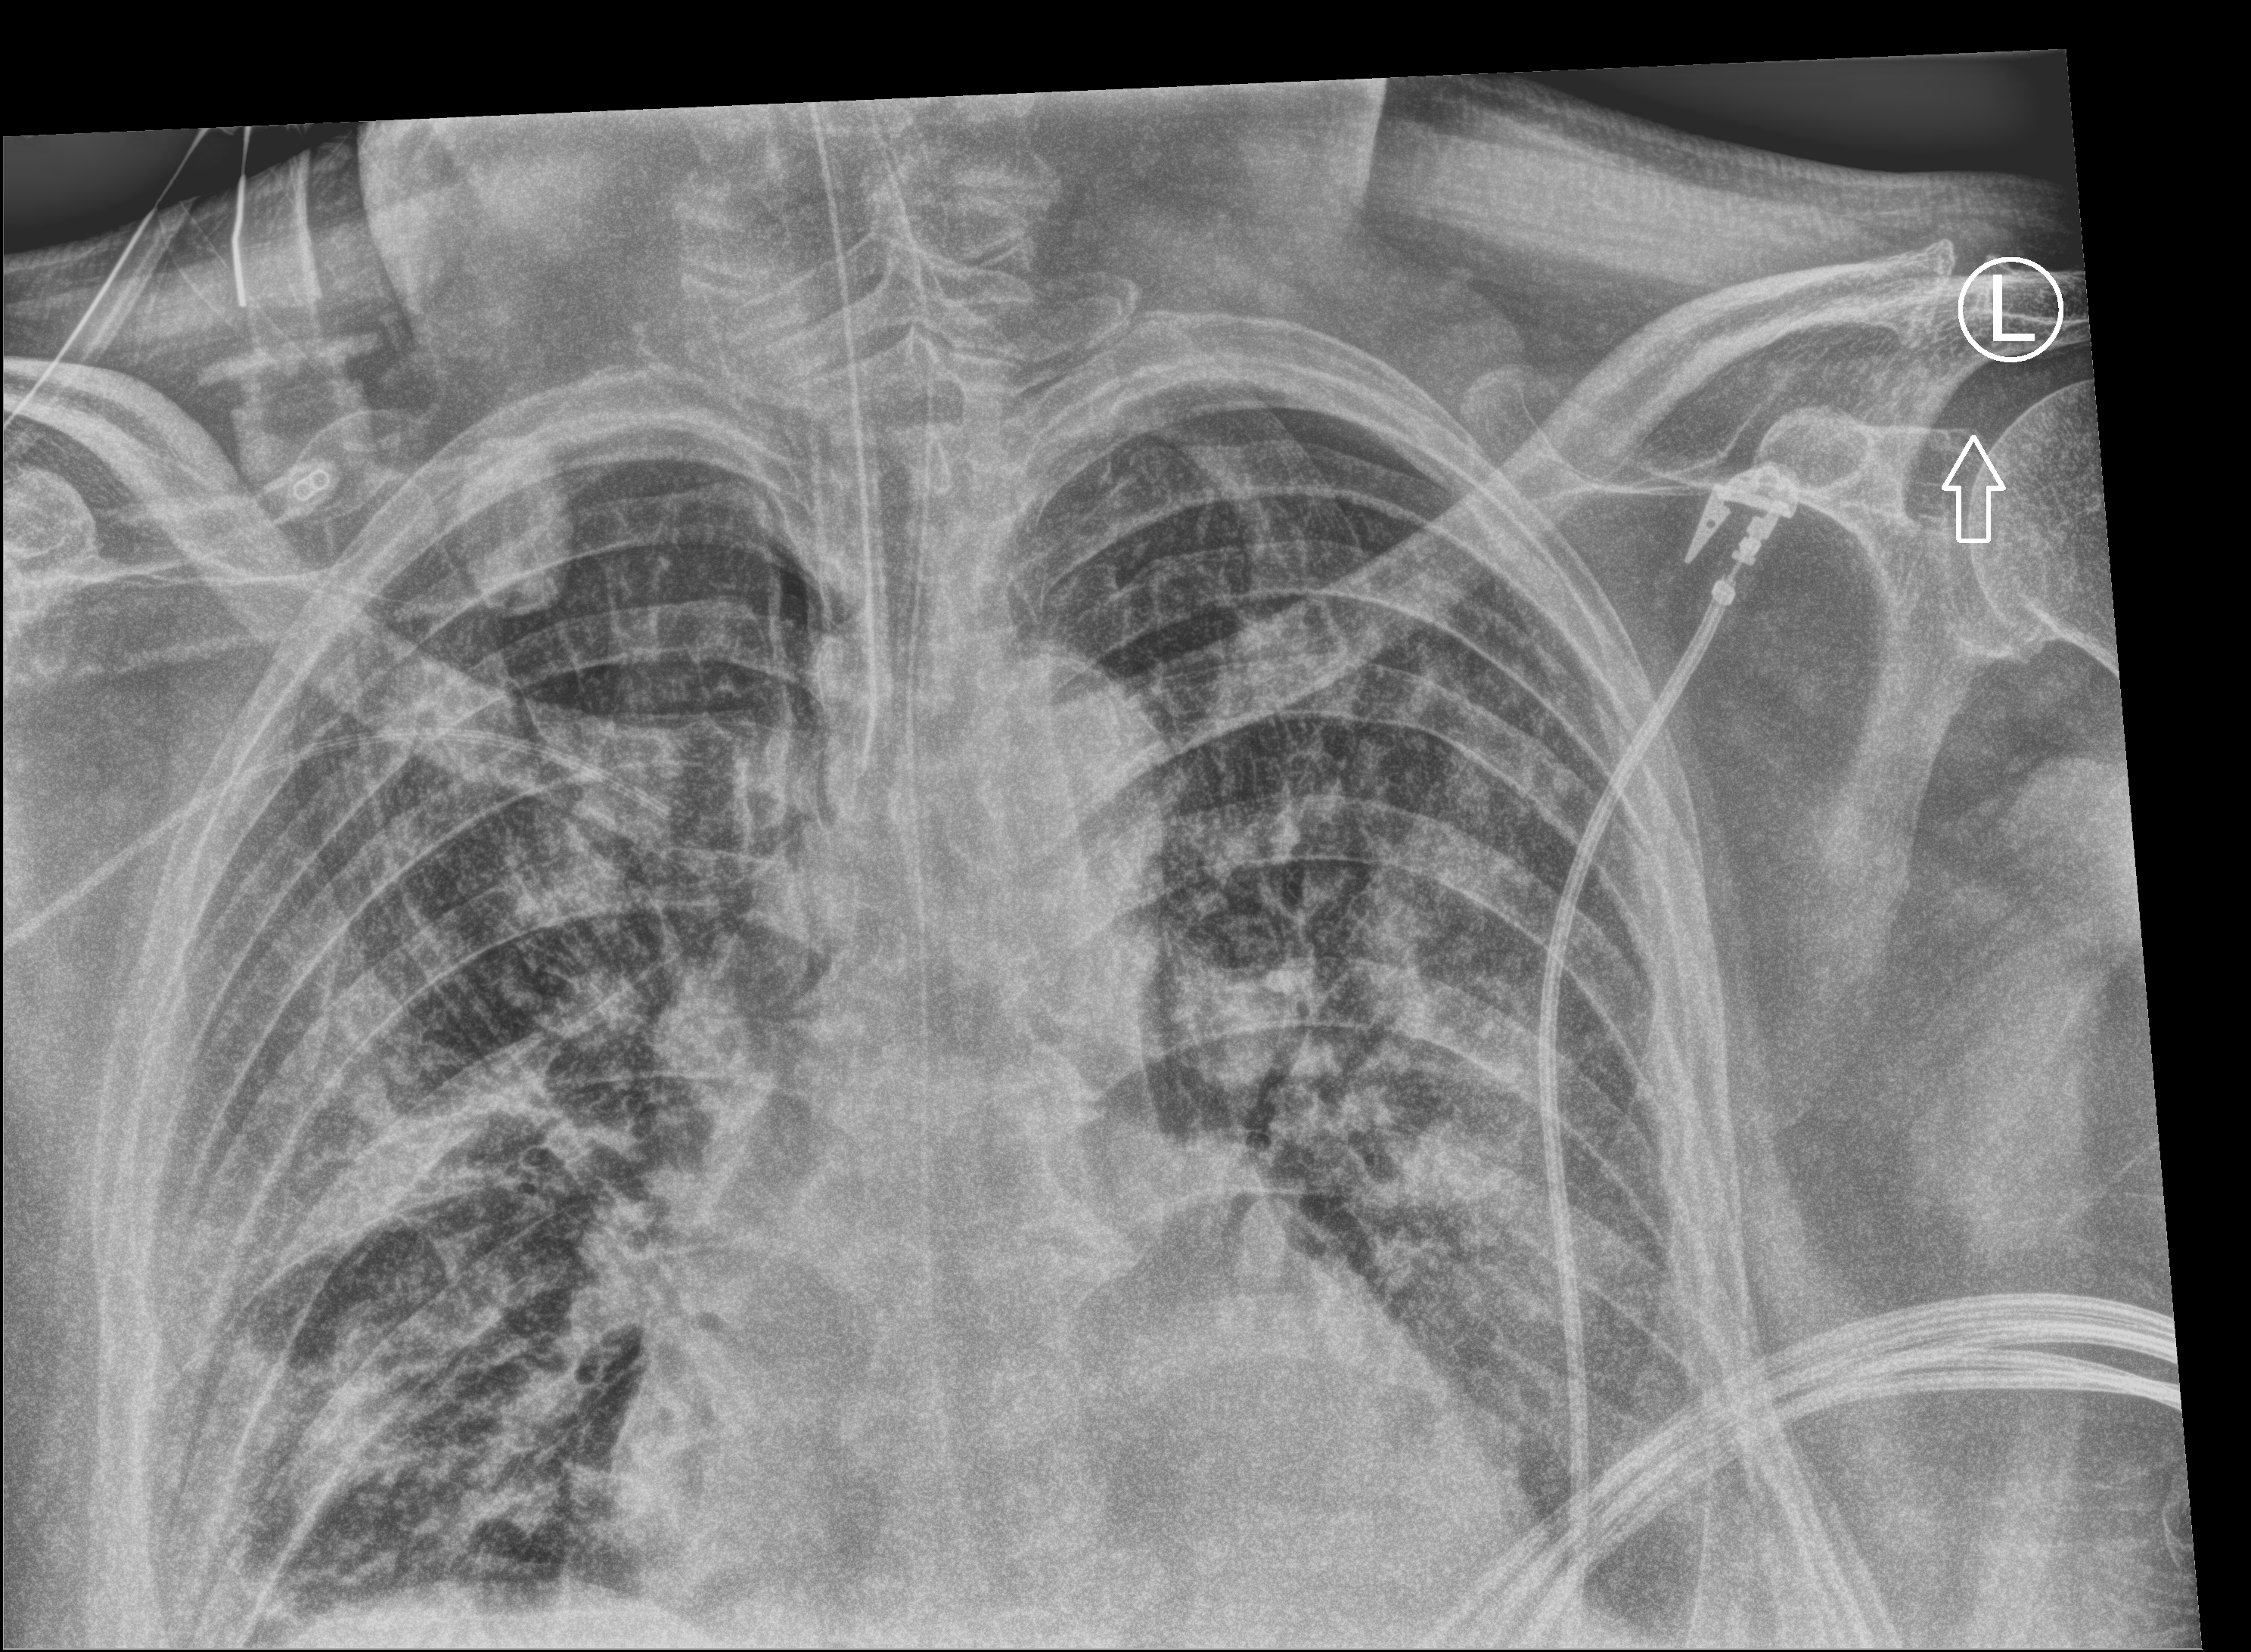
Bedside chest radiograph (computed radiography); anteroposterior (AP) projection. Male patient hospitalised with COVID-19, age 60–74 years.
Admission-level facts for this patient (not findings on this image; timing relative to this image not recorded): chronic kidney disease (admission record): no; admitted to intensive care during this hospital stay: yes.